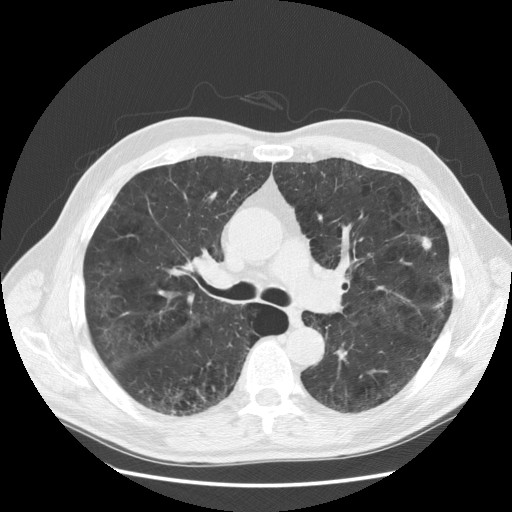
Low-dose screening chest CT, one axial slice; position 95 of 163 along the scan axis; reconstruction kernel STANDARD; 120 kVp; lung window (W 1500 / L -600 HU); 2.5 mm slice thickness; 512 × 512 image matrix.
Structures marked on this image (expert manual segmentation):
- lesion 1 (tumor, upper lobe of left lung): bounding box <421,236,432,249> (left, top, right, bottom; pixels)